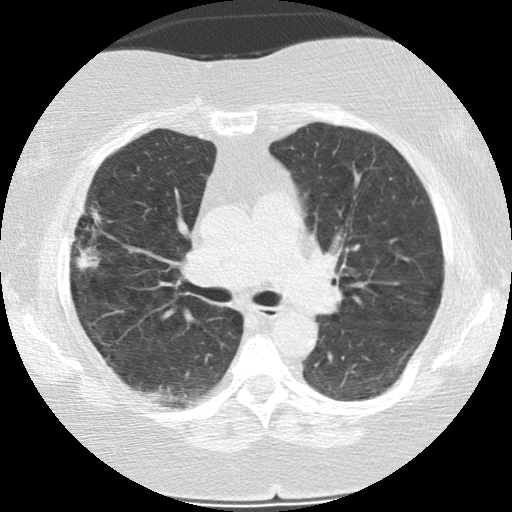
Chest CT (low-dose screening protocol), one axial image. First (baseline) screen. Lung window (W 1500 / L -600 HU). 2.5 mm slice thickness. Standard (soft-tissue) reconstruction kernel (STANDARD). 120 kVp. Female participant, aged 73 years at enrolment. Former smoker at enrolment.
• Lesion marked by an expert reader, box from (x=58, y=214) to (x=114, y=278) px.
• Screening reader's record for this exam (one nodule recorded; not confirmed to be the boxed lesion): non-calcified nodule or mass ≥4 mm, right upper lobe, 21 × 14 mm, poorly defined margins, soft tissue attenuation.
• Later outcome: lung cancer diagnosed 482 days after this screen (after the second annual screen) — bronchiolo-alveolar adenocarcinoma, NOS, right upper lobe, moderately differentiated (G2), stage IIIB (AJCC 6th edition), 21 mm at pathology.